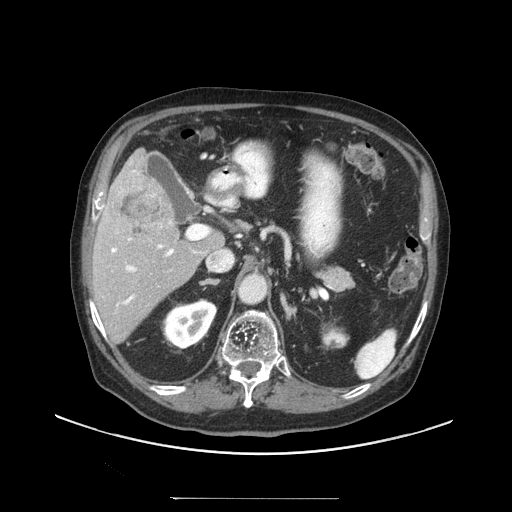
Contrast-enhanced abdominal CT (liver protocol), one axial slice; slice 58 of 97 in the series (ordered by position); reconstruction kernel STANDARD; 140 kVp; soft-tissue window (W 400 / L 40 HU); 512 × 512 image matrix, field of view 450 × 450 mm. From the clinical record (not read from this slice): diagnosis: hepatocellular carcinoma (patient treated with transarterial chemoembolisation; whether this scan precedes or follows treatment is not stated here); TNM stage (as recorded): Stage-IIIC; Child-Pugh class: A; tumour differentiation: well differentiated; tumour nodularity: uninodular.
Annotated regions visible in this slice (semi-automatically segmented with operator editing):
- liver parenchyma outside the tumour (the mass and vessels are separate outlines, so this box may not span the whole liver): bounding box (x1, y1, x2, y2) in pixels: (92, 148, 224, 342)
- mass: (108, 177, 172, 239)
- liver vessels: (111, 170, 196, 306)